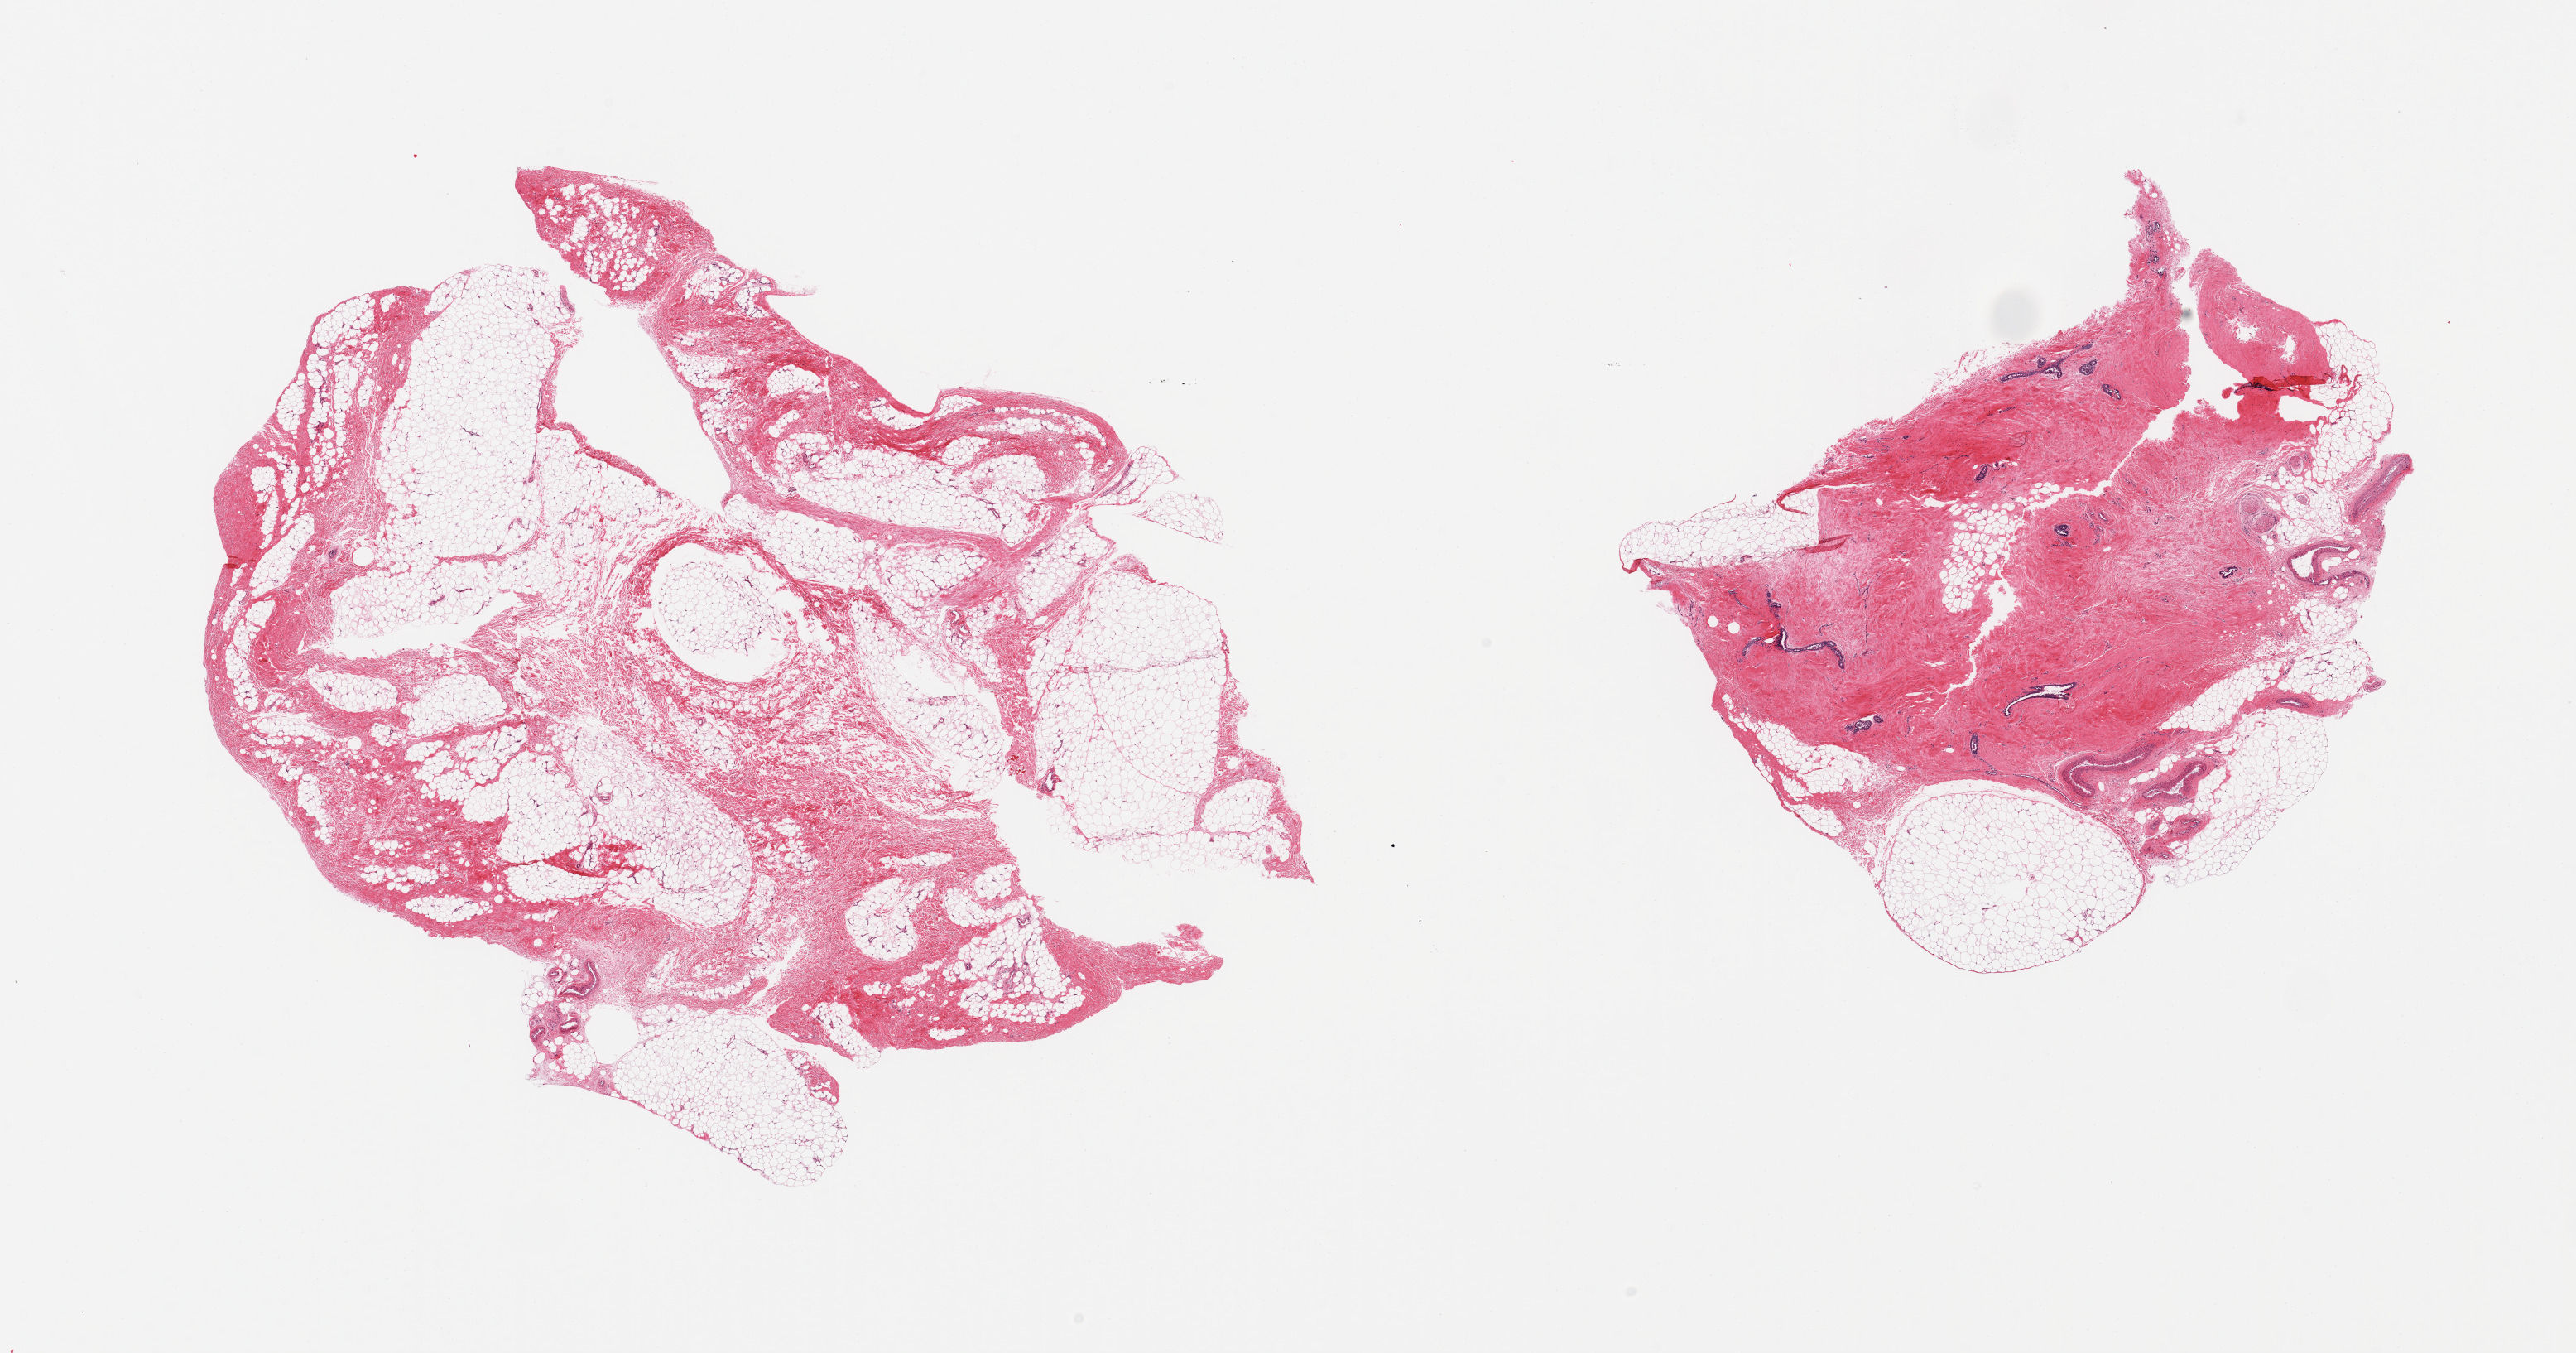
Digitized H&E-stained section, brightfield — shown as a low-resolution overview of the whole scanned area (about 24.6 x 12.9 mm), PAXgene-fixed, paraffin-embedded tissue, sampled site (target tissue): breast, donor tissue sample. Male donor.
• reviewer comment on this tissue sample: 2 pieces; 1 is fat admixed with fibrocollagenous stroma, 2nd is 20% fat with 80% dense fibrous stroma with scattered ducts, focus of nerves/larger vessels